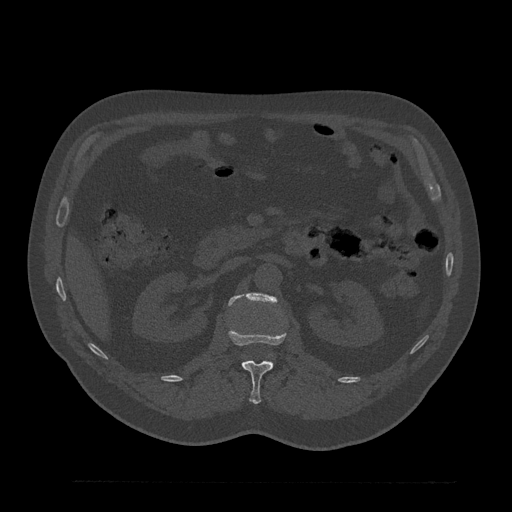
CT including the spine, one axial slice. Slice 146 of 797 in the series (ordered by position). Bone window (W 1800 / L 400 HU). 0.5 mm slice thickness. 512 × 512 image matrix, field of view 430 × 430 mm. Patient: male, 61 years. From the clinical record (not read from this slice): primary cancer: prostate.
Structures marked on this image (semi-automatic segmentation, software-assisted and operator-edited):
- L1 vertebra: box from (x=228, y=326) to (x=287, y=405) px
- L2 vertebra: (x=228, y=293)–(x=277, y=306)